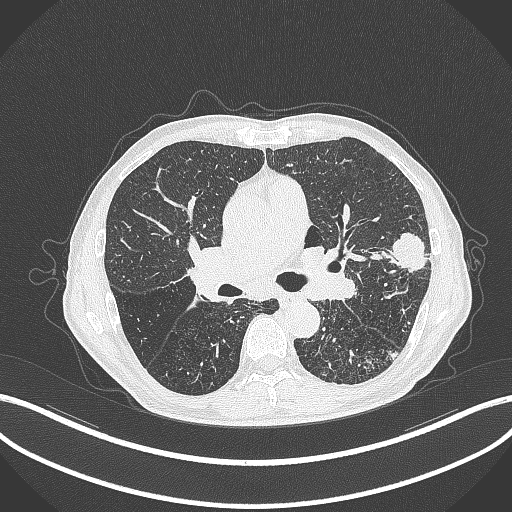
Chest CT, one axial slice. Slice 243 of 463 in the series (ordered by position). Reconstruction kernel B70f. Lung window (W 1500 / L -600 HU). 1 mm slice thickness. 512 × 512 image matrix, field of view 400 × 400 mm. Patient: male, 74 years. From the clinical record (not read from this slice): clinical TNM (as recorded): T2a N1 M0.
Structures marked on this image (rectangle marked by the reading radiologist):
- lung tumour (recorded histology: adenocarcinoma): bounding box <379,234,426,275> (left, top, right, bottom; pixels)